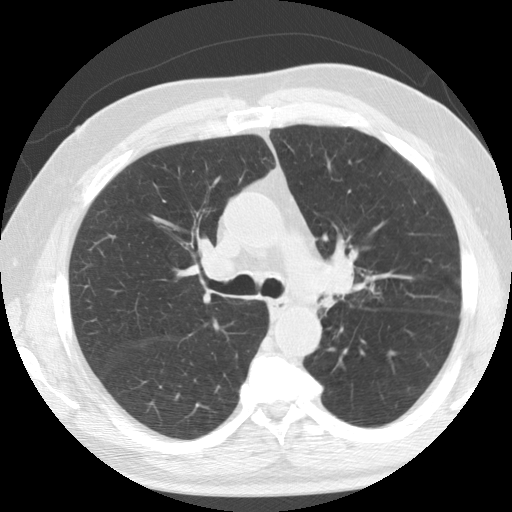
Chest CT (low-dose screening protocol), one axial image; second screening round (one year after baseline); lung window (W 1500 / L -600 HU); 2.5 mm slice thickness; 120 kVp. Male participant, aged 74 years at enrolment. Current smoker at enrolment.
• Lesion marked by an expert reader, box from (x=301, y=245) to (x=367, y=313) px.
• Screening reader's record for this exam: no non-calcified nodule ≥4 mm recorded.
• Official screen result: positive, other.
• Later outcome: lung cancer diagnosed 274 days after this screen — non-small cell carcinoma, left upper lobe, poorly differentiated (G3), stage IIB (AJCC 6th edition).